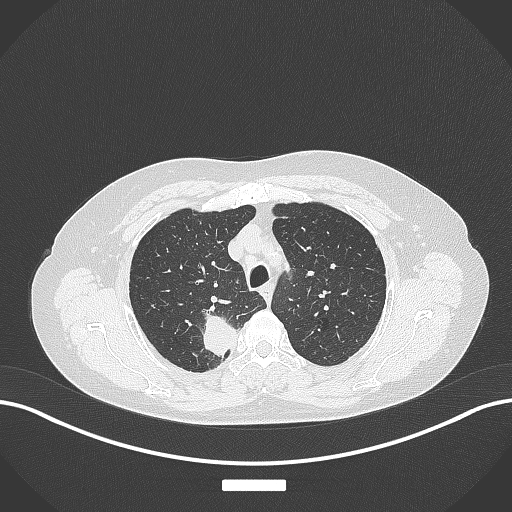
Chest CT, one axial slice; position 304 of 357 along the scan axis; reconstruction kernel B70f; 120 kVp; lung window (W 1500 / L -600 HU); 1 mm slice thickness; 512 × 512 image matrix, field of view 400 × 400 mm. Patient: female, 62 years. Case-level facts recorded for this patient, not image findings: clinical TNM (as recorded): T1c N1 M0.
Structures marked on this image (rectangle marked by the reading radiologist):
- lung tumour (recorded histology: squamous cell carcinoma): bounding box [x1, y1, x2, y2] px = [197, 307, 236, 361]